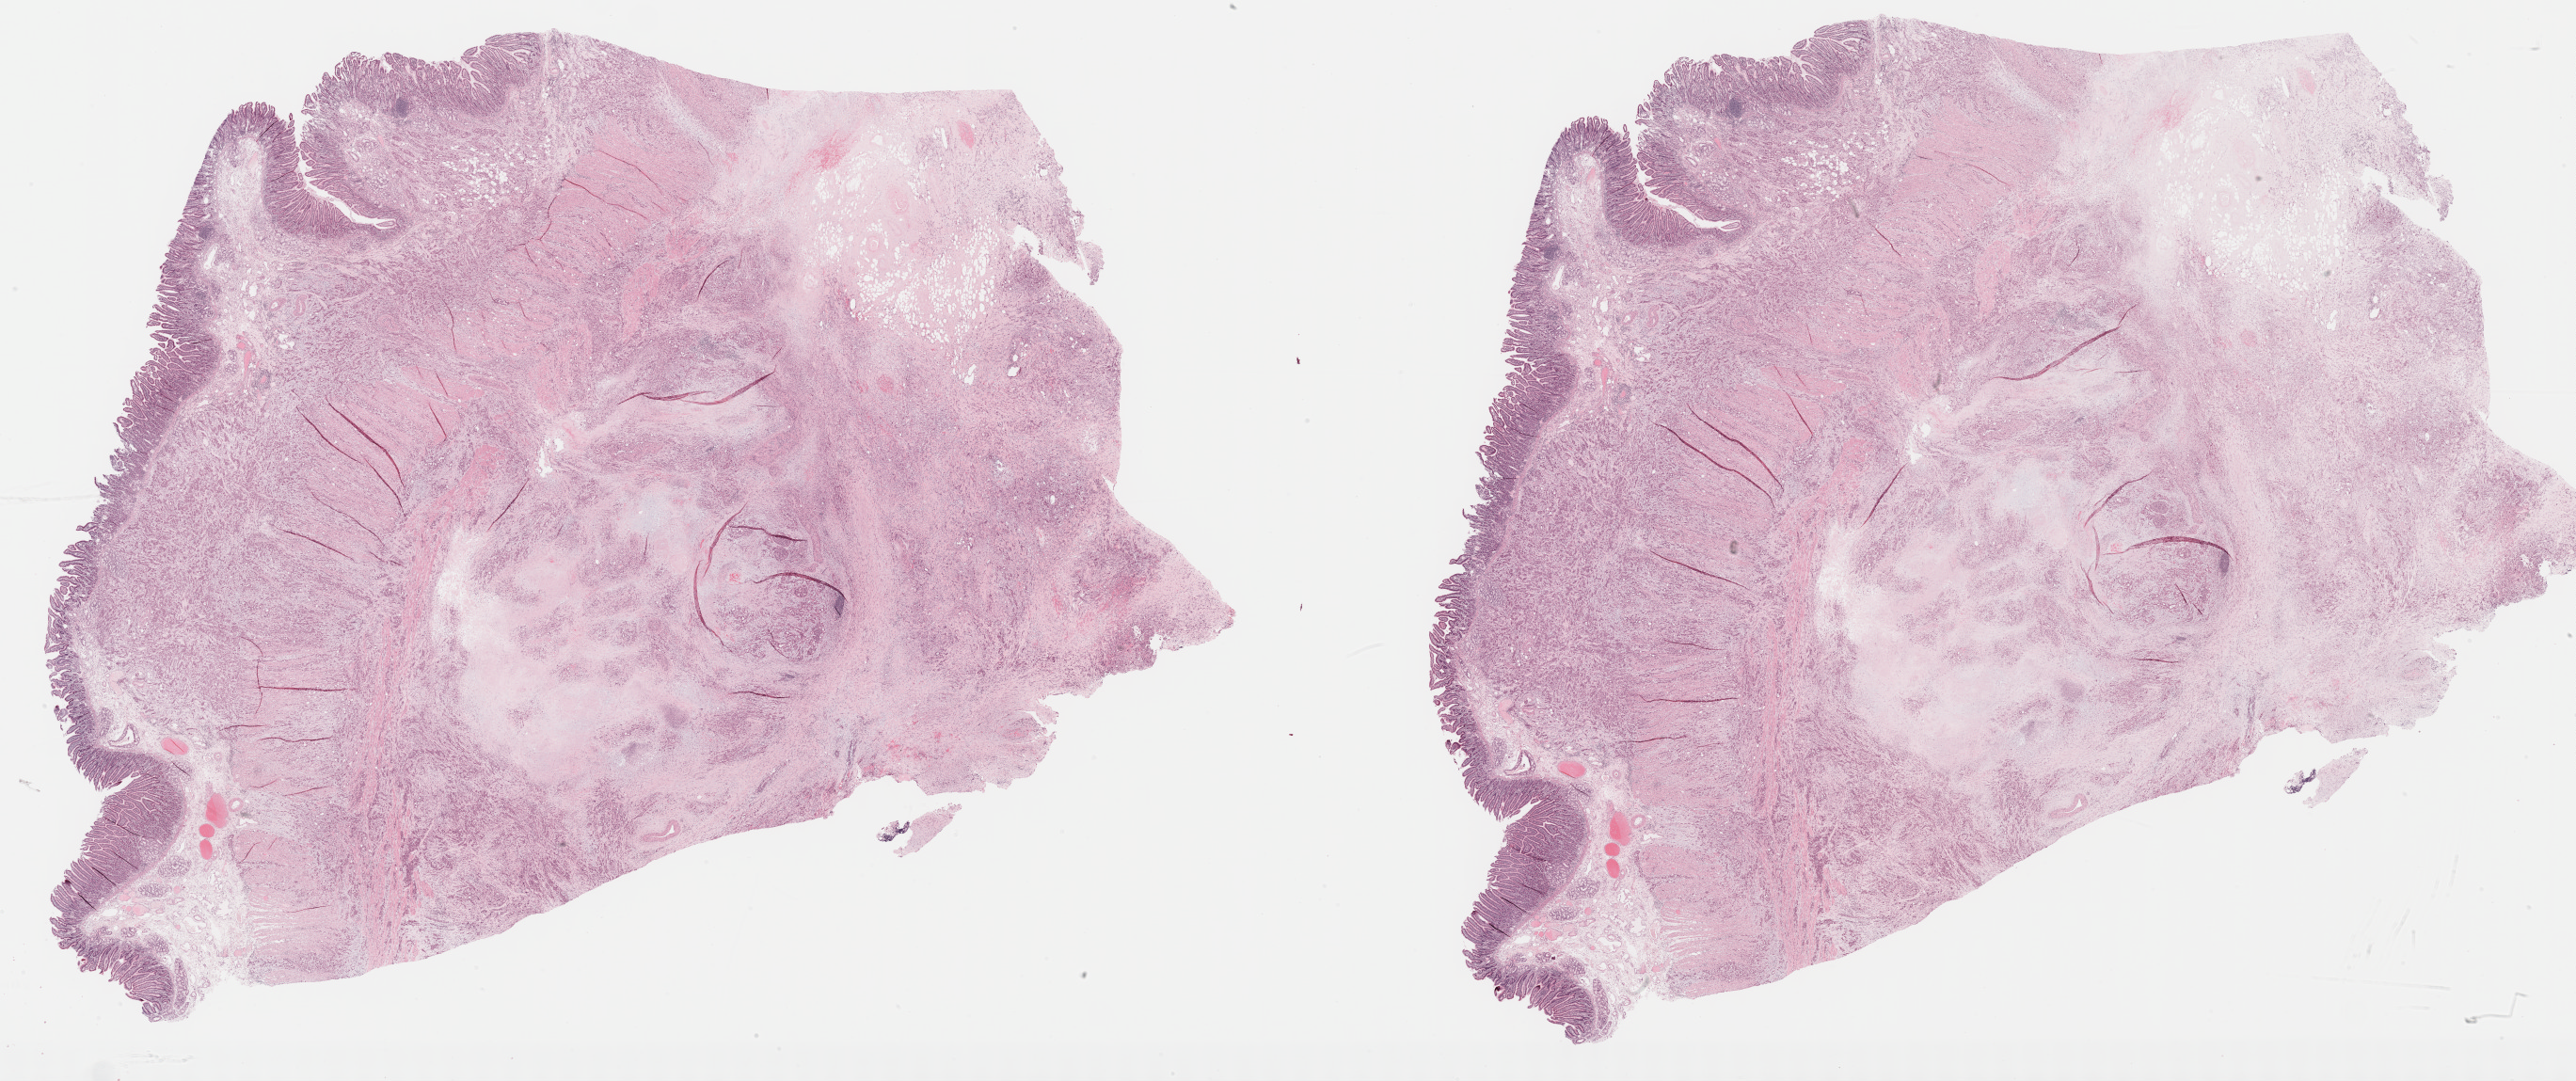
H&E-stained whole-slide image, low-resolution overview of the scanned area, about 44.3 x 18.6 mm (slide scanned at 40x); formalin-fixed paraffin-embedded (FFPE) diagnostic section; pancreas, primary tumour sample. Female, age 56 years at initial diagnosis.
Histologic diagnosis: Infiltrating duct carcinoma, NOS (head of pancreas).